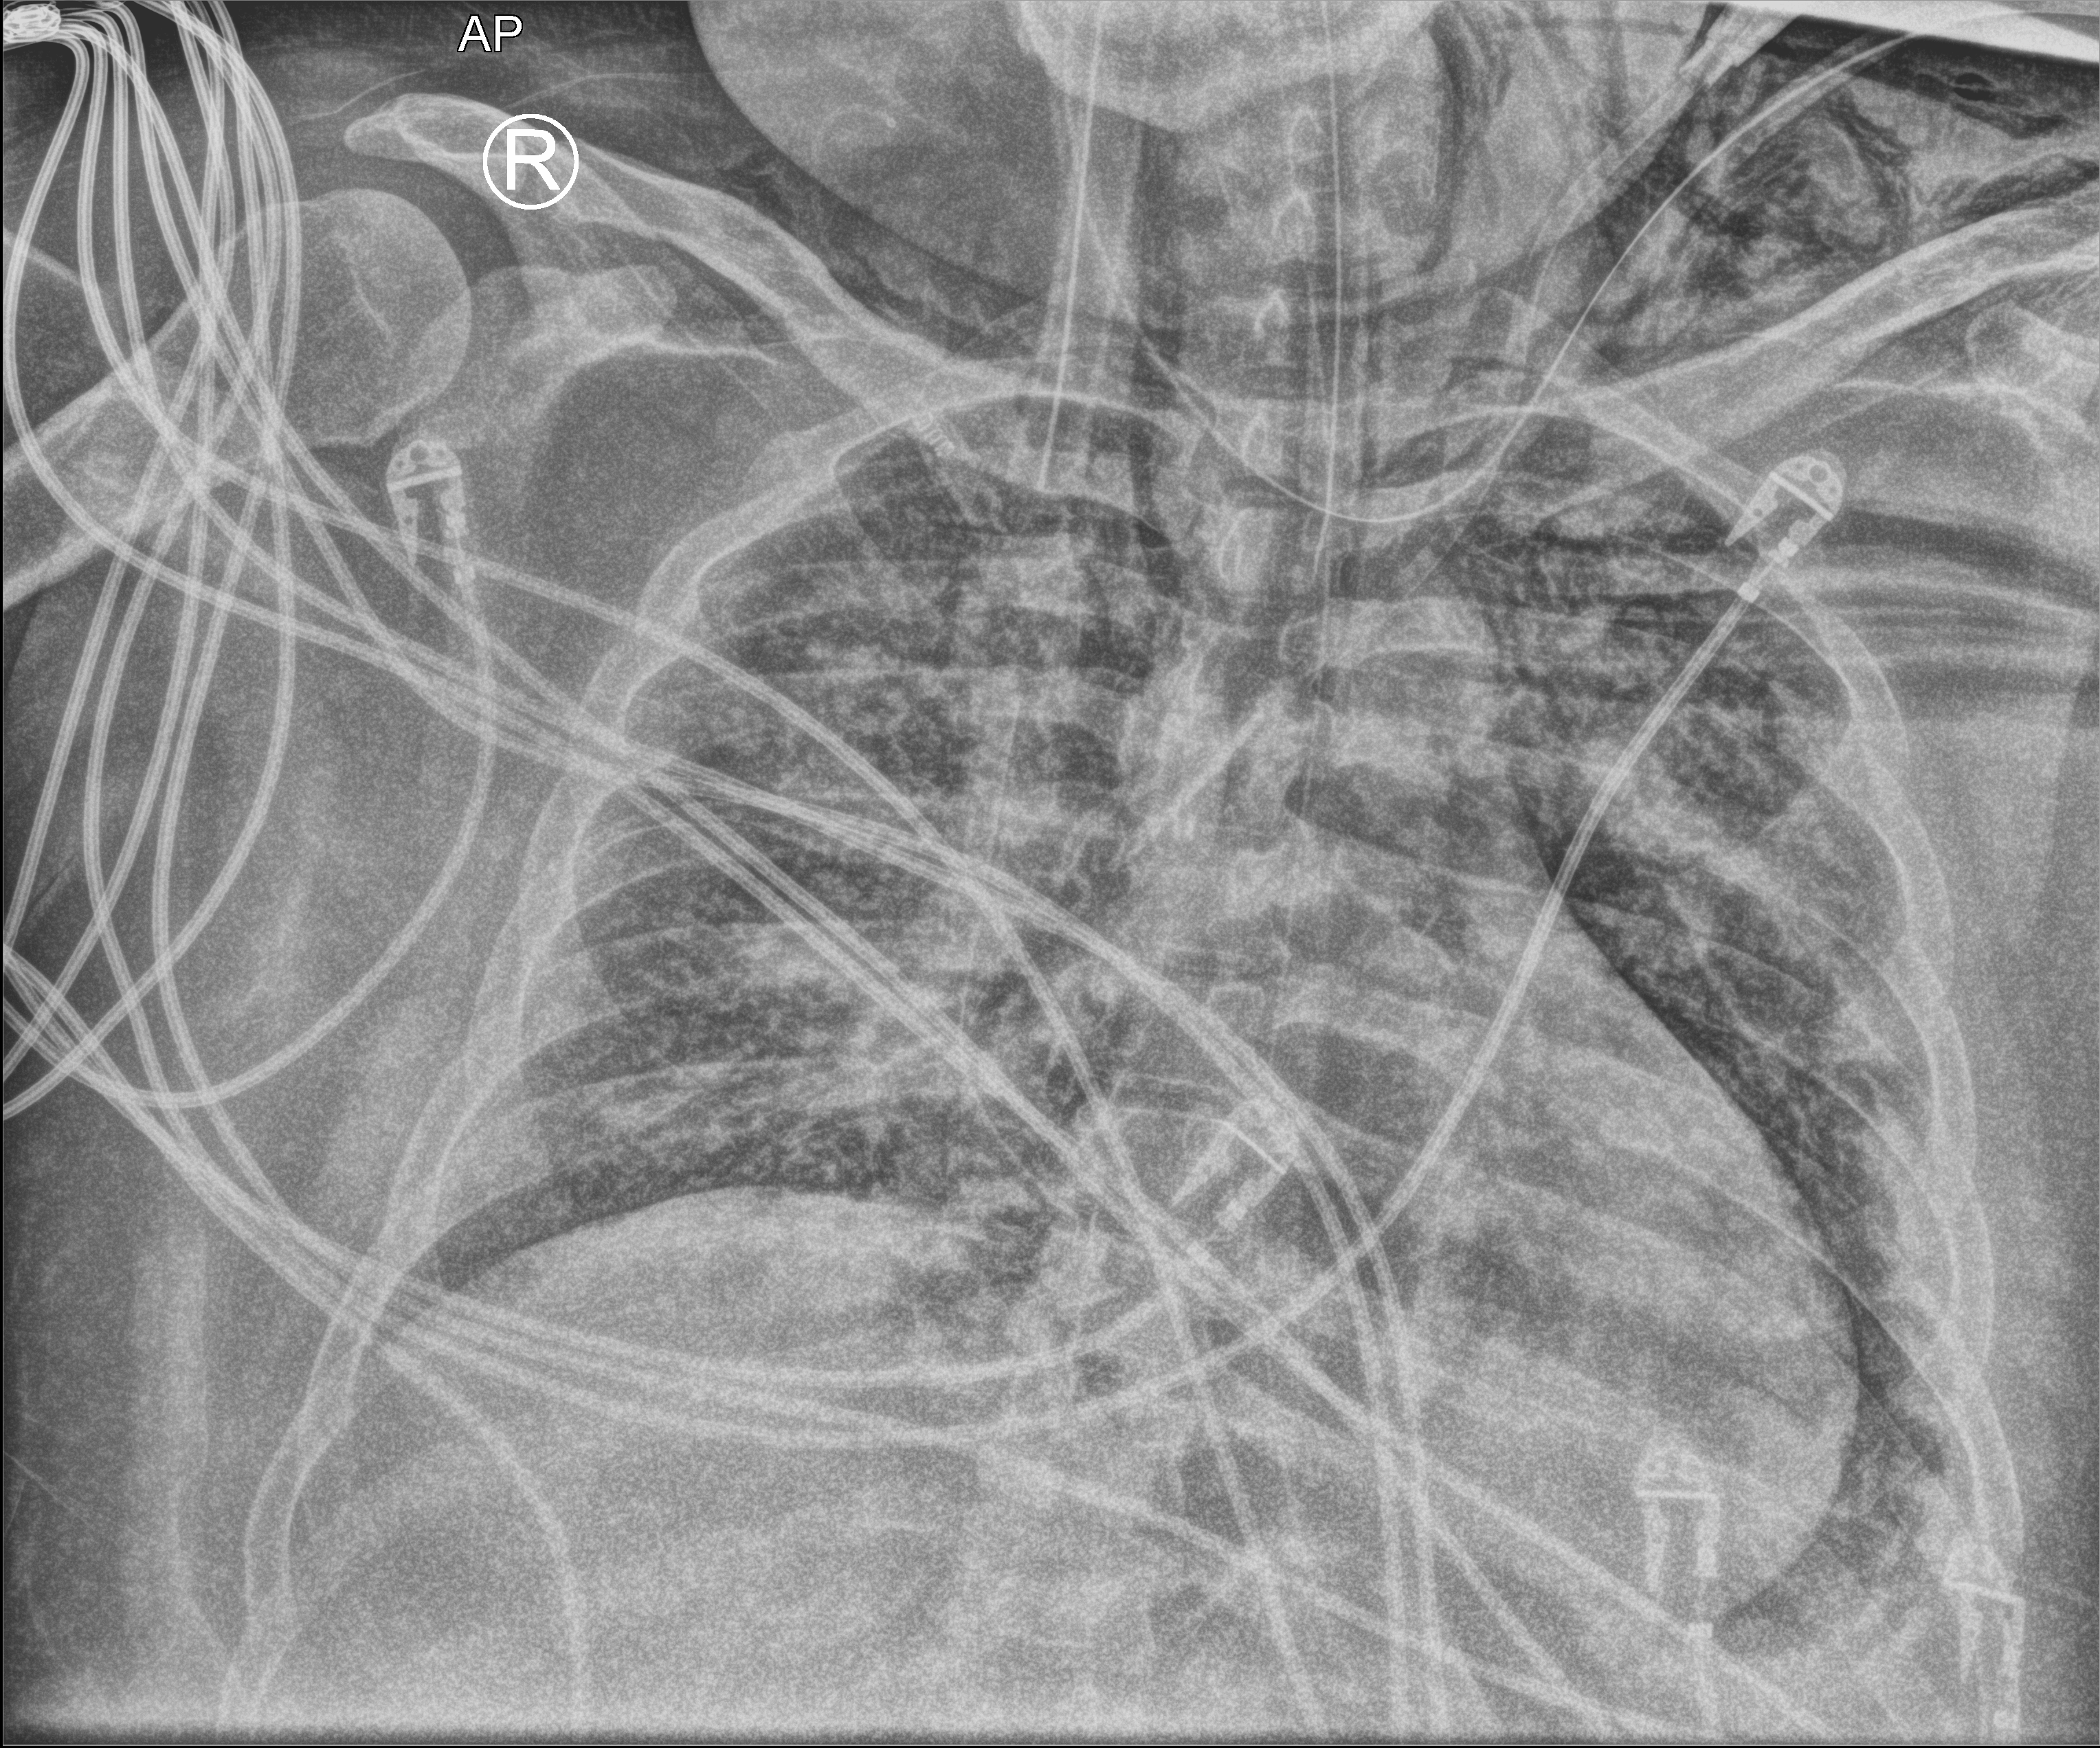
Portable chest radiograph; anteroposterior (AP) projection. Patient hospitalised with COVID-19, aged 18–59 years.
Admission-level facts for this patient (not findings on this image; timing relative to this image not recorded): mechanically ventilated during this hospital stay: yes; diabetes (admission record): no; admitted to intensive care during this hospital stay: yes.